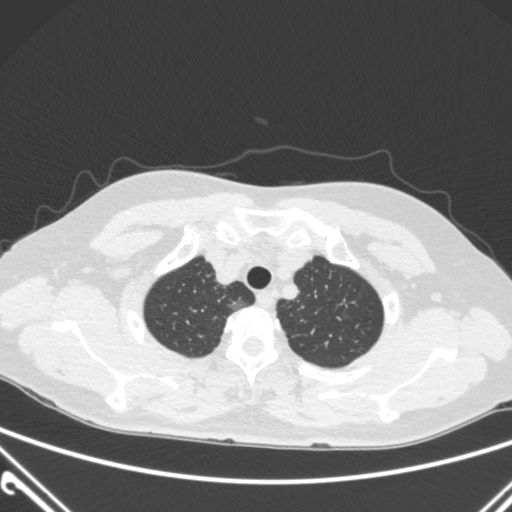
Chest CT, one axial slice. Slice 246 of 300 in the series (ordered by position). Lung window (W 1500 / L -600 HU). 1 mm slice thickness. 512 × 512 image matrix, field of view 350 × 350 mm. Female patient, age 54 years. From the clinical record (not read from this slice): clinical TNM (as recorded): T1a N0 M0; histopathological grade: G1.
Outlined on this slice (rectangle marked by the reading radiologist):
- lung tumour (recorded histology: adenocarcinoma): box from (x=224, y=295) to (x=255, y=318) px